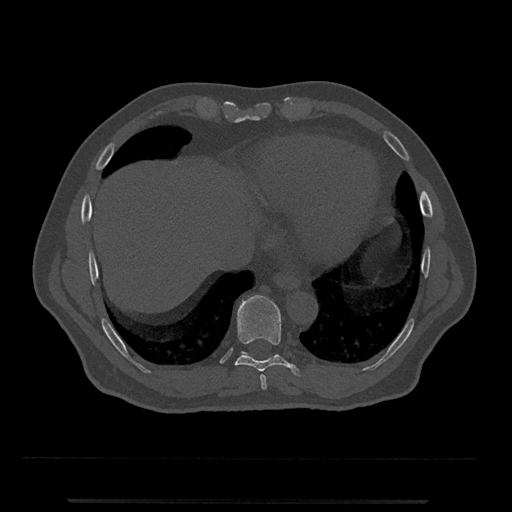
CT including the spine, one axial slice; position 568 of 797 along the scan axis; reconstruction kernel Br40s/3; bone window (W 1800 / L 400 HU); 0.5 mm slice thickness; 512 × 512 image matrix. Patient: male, 63 years. From the clinical record (not read from this slice): primary cancer: prostate.
Structures marked on this image (semi-automatic segmentation, software-assisted and operator-edited):
- T10 vertebra: bounding box [x1, y1, x2, y2] px = [241, 351, 277, 355]
- T8 vertebra: [260, 375, 267, 390]
- T9 vertebra: [235, 295, 300, 376]